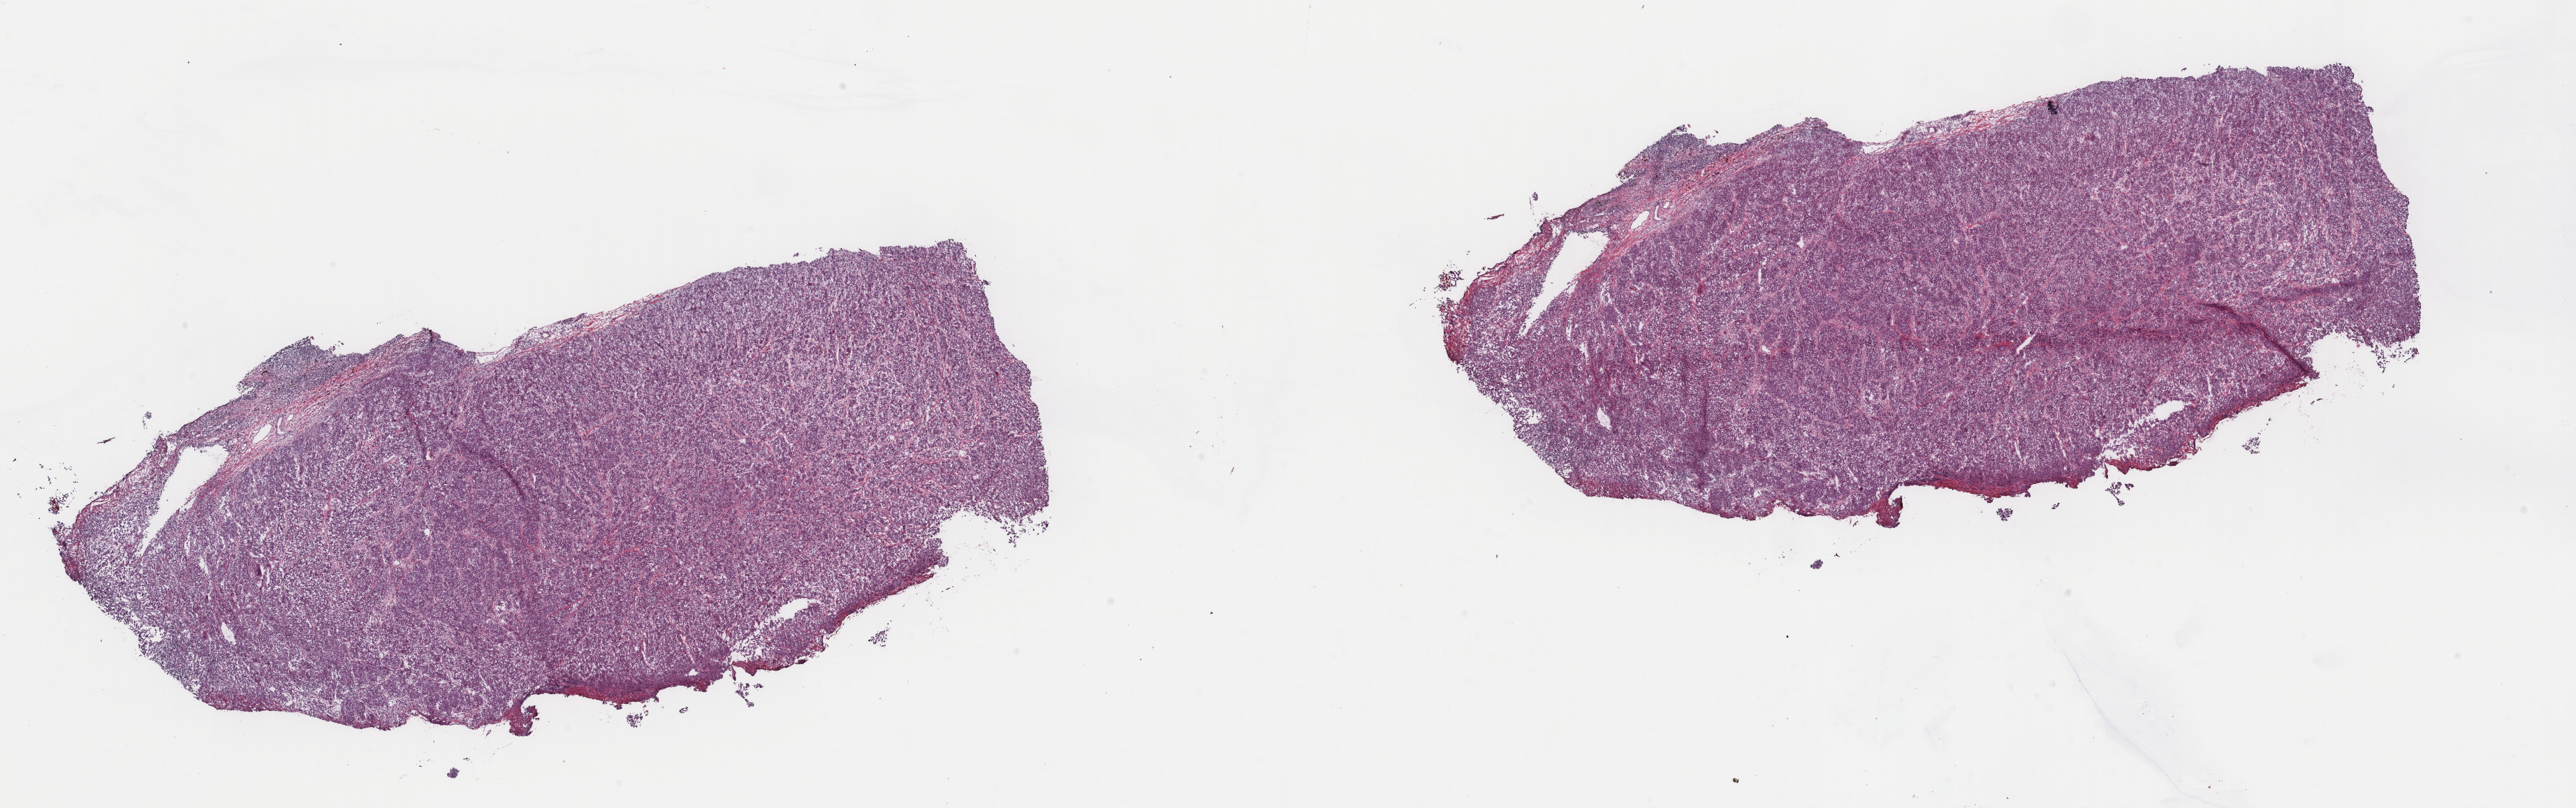
Hematoxylin and eosin (H&E) stained whole-slide image, whole scanned area (about 29.3 x 9.2 mm, slide scanned at 40x) shown as a low-resolution overview; frozen section; sample: primary tumour, skin. Female patient; age at initial diagnosis 76 years. Composition of this section per pathologist review: tumour cells 99%, tumour nuclei 96%, normal cells 0%, stromal cells 1%, necrosis 0%. Inflammatory infiltration, as recorded: lymphocyte infiltration 0%, monocyte infiltration 0%, neutrophil infiltration 0%.
* AJCC pathologic stage: IIC (7th edition)
* pathologic diagnosis: Malignant melanoma, NOS